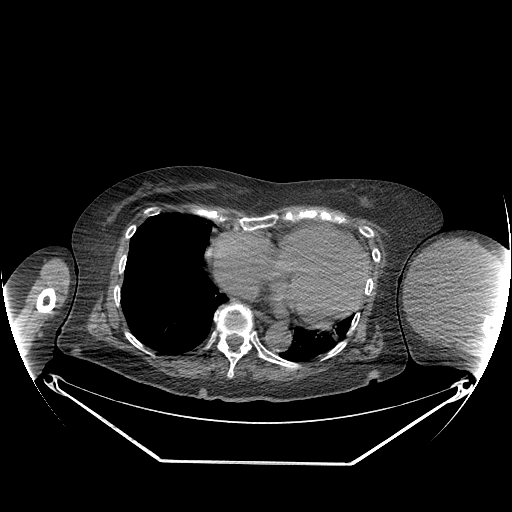
CT of an extremity soft-tissue mass (from a PET/CT study), one axial slice; 140 kVp; soft-tissue window (W 400 / L 40 HU); 3.75 mm slice thickness; 512 × 512 image matrix. Female patient. Case-level facts recorded for this patient, not image findings: histological type: pleiomorphic leiomyosarcoma; grade: high; site of the primary tumour: left biceps.
Annotated regions visible in this slice (expert contour drawn on MRI and transferred to this co-registered scan by the dataset authors):
- gross tumour volume including surrounding oedema: box from (x=406, y=238) to (x=496, y=330) px
- gross tumour volume (mass): (x=406, y=240)–(x=496, y=328)